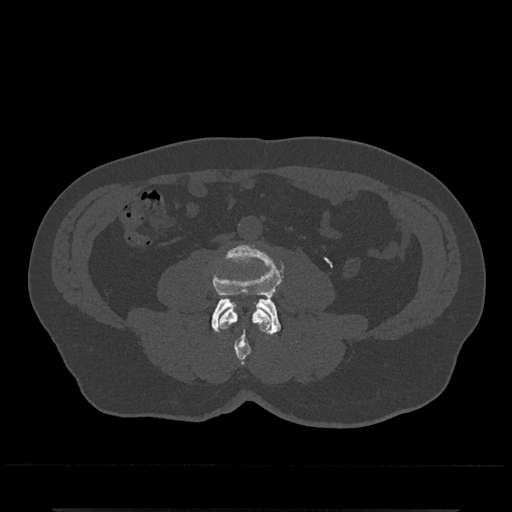
CT including the spine, one axial slice; slice 184 of 797 in the series (ordered by position); 120 kVp; bone window (W 1800 / L 400 HU); 0.5 mm slice thickness; 512 × 512 image matrix. Patient: male, 67 years. From the clinical record (not read from this slice): primary cancer: prostate.
Outlined on this slice (semi-automatically segmented with operator editing):
- L3 vertebra: bounding box (x1, y1, x2, y2) in pixels: (218, 307, 272, 365)
- L4 vertebra: (212, 245, 282, 335)